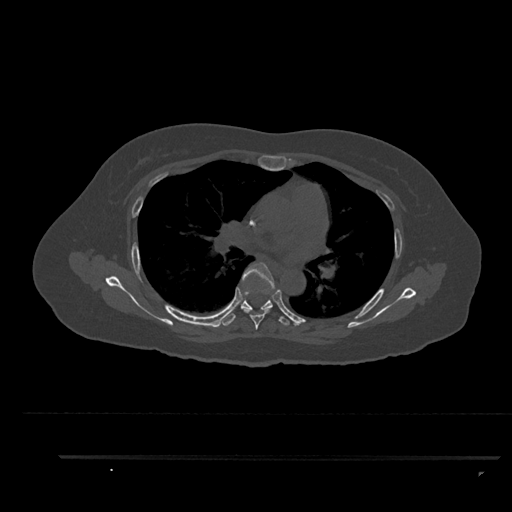
CT including the spine, one axial slice. Position 581 of 797 along the scan axis. Reconstruction kernel Br40s/3. Bone window (W 1800 / L 400 HU). 0.5 mm slice thickness. 512 × 512 image matrix. Patient: female, 44 years. From the clinical record (not read from this slice): primary cancer: renal; vertebrae with lytic lesions (as recorded): L1.
Structures marked on this image (semi-automatically segmented with operator editing):
- T5 vertebra: box from (x=240, y=262) to (x=275, y=330) px
- T6 vertebra: (x=223, y=291)–(x=290, y=326)